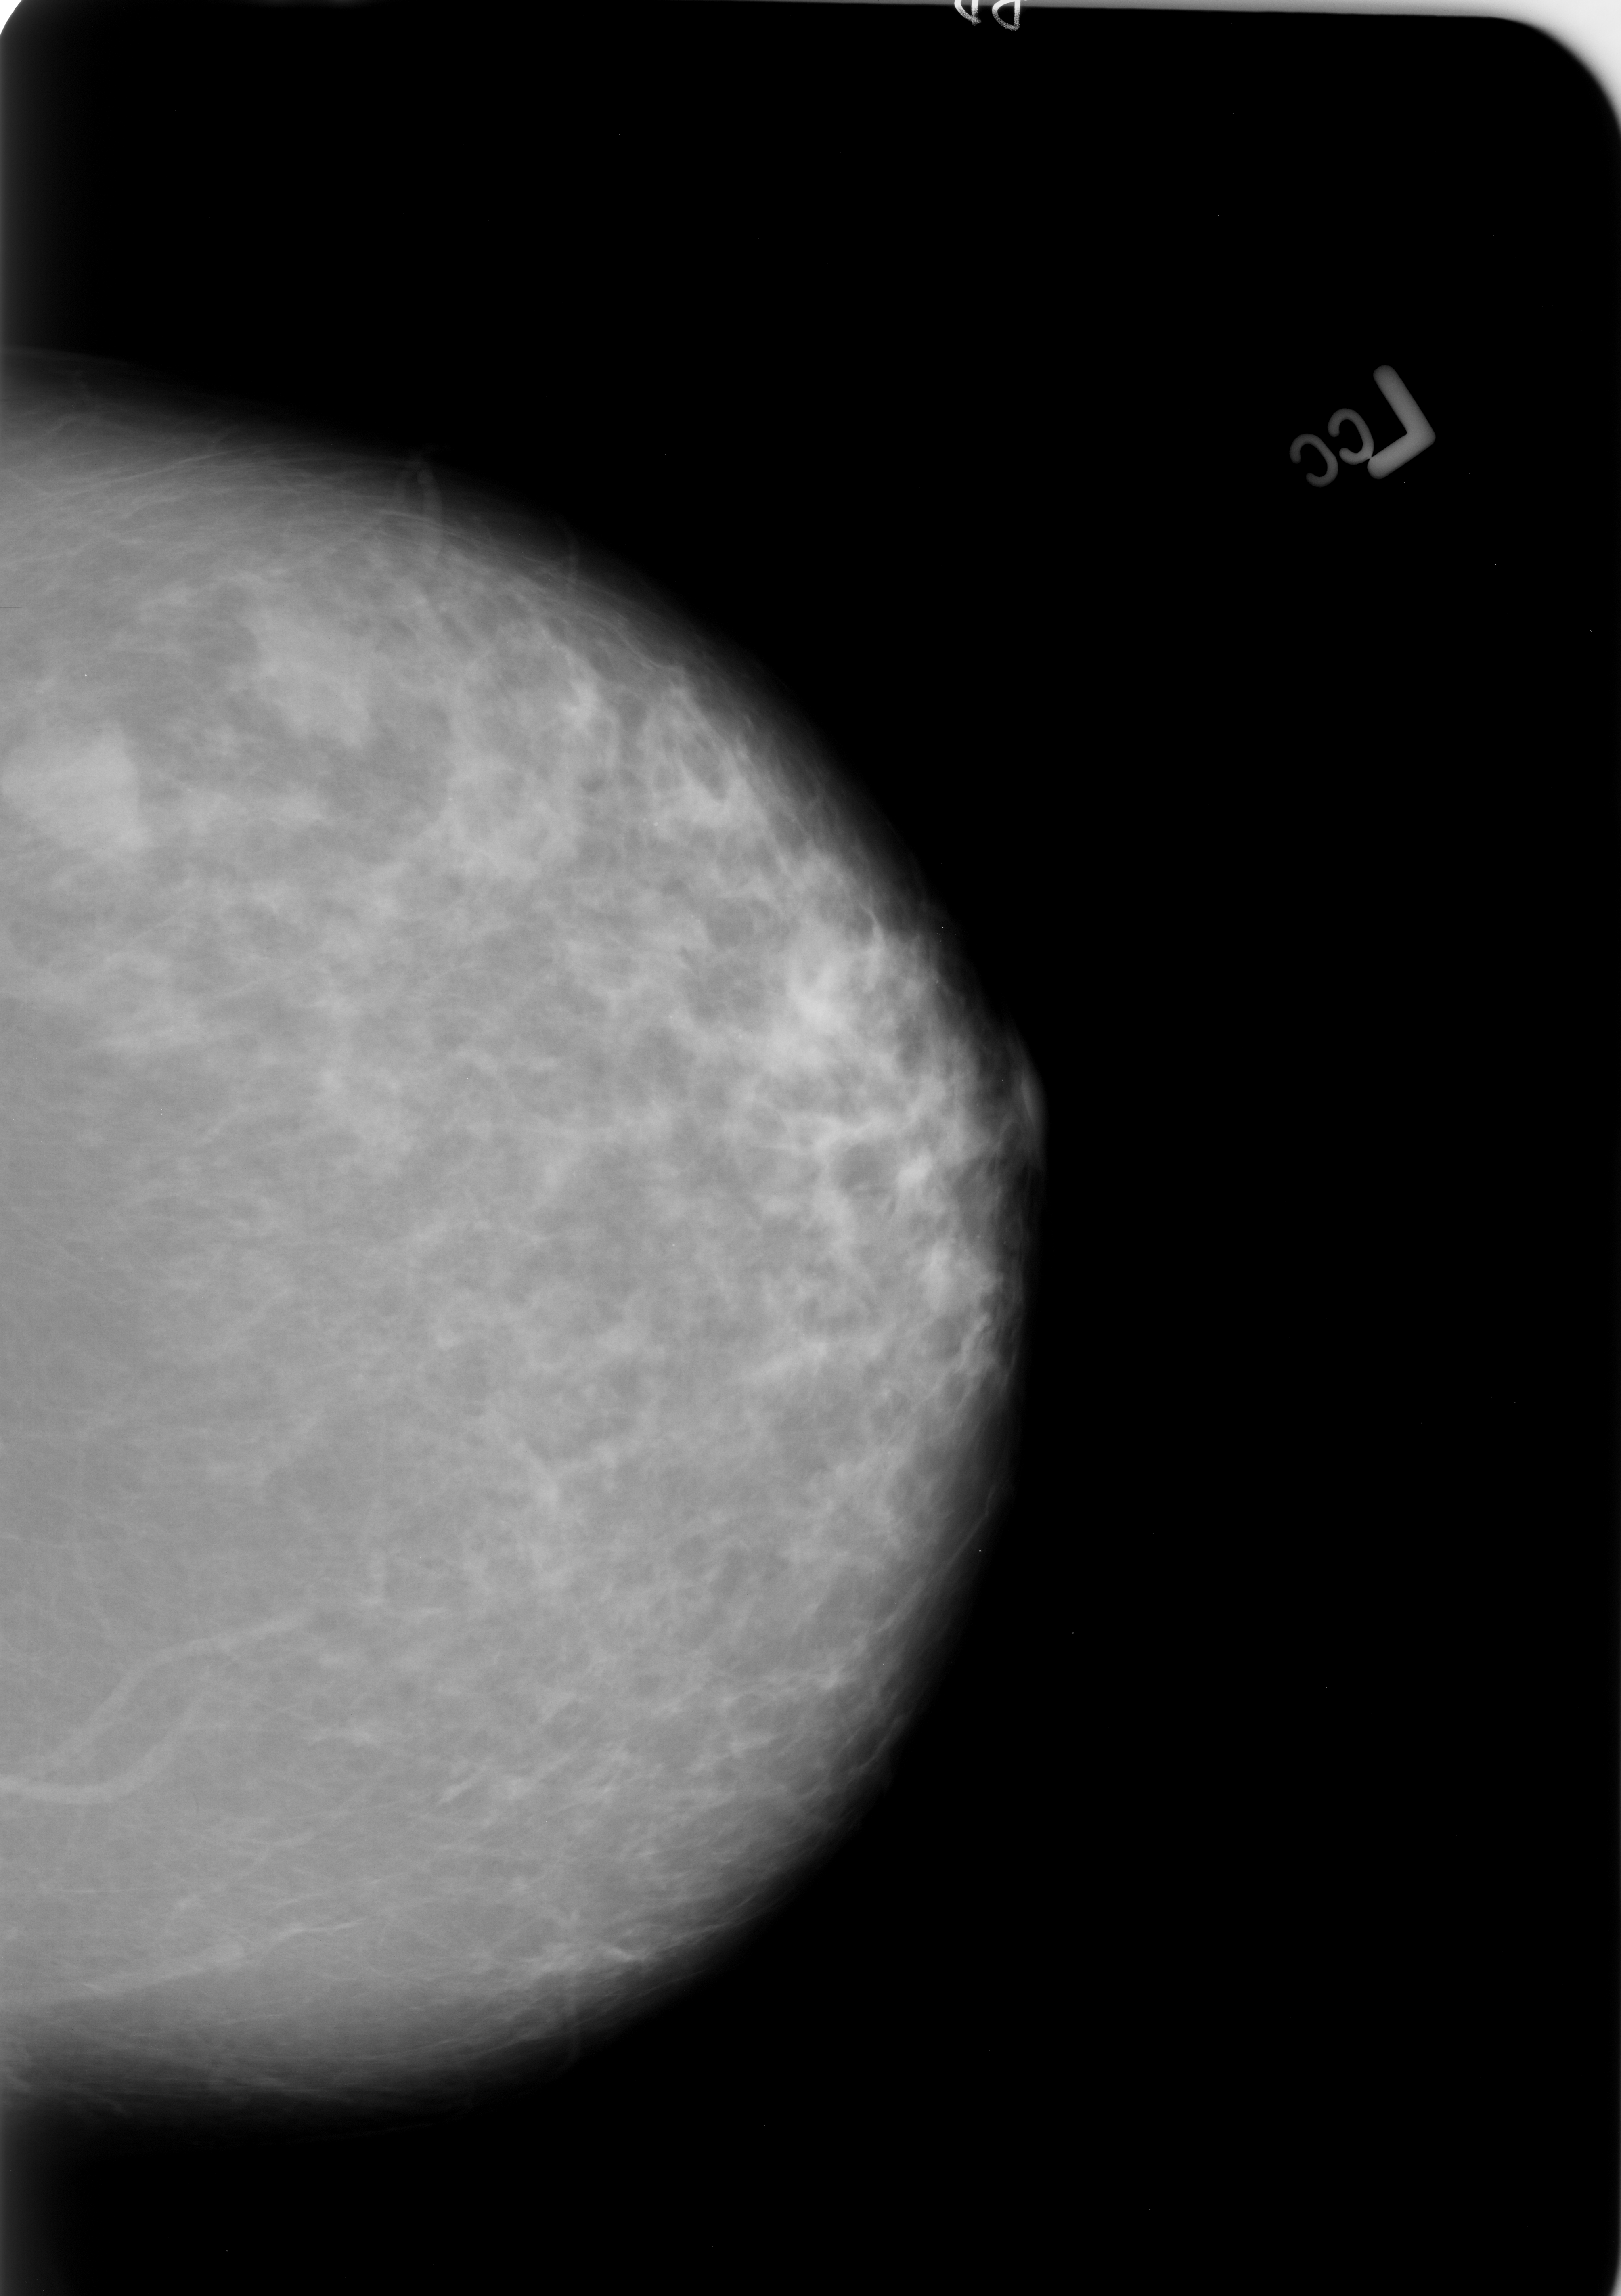
Scanned film-screen mammogram; left breast; CC view; breast composition: scattered fibroglandular densities (BI-RADS density category 2 of 4); 1621 × 2296 image matrix.
Expert-marked regions of interest on this image (one box per marked abnormality):
- mass, shape lobulated, margins circumscribed; BI-RADS assessment category 4; pathology result (as recorded, not read from the image): benign: bounding box [x1, y1, x2, y2] px = [23, 732, 142, 859]